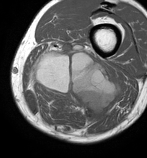
MRI of an extremity soft-tissue mass, one axial slice; slice 31 of 86 in the series (ordered by position); MR volume resampled by the dataset authors to the PET/CT grid (not the native acquisition matrix); 3.27 mm slice thickness; 147 × 158 image matrix, field of view 144 × 154 mm. Male patient. Case-level facts recorded for this patient, not image findings: histological type: undifferentiated pleomorphic liposarcoma; grade: high; site of the primary tumour: left thigh.
Outlined on this slice (expert contour drawn on MRI and transferred to this co-registered scan by the dataset authors):
- gross tumour volume including surrounding oedema: box from (x=28, y=40) to (x=120, y=125) px
- gross tumour volume (mass): (x=35, y=53)–(x=115, y=116)